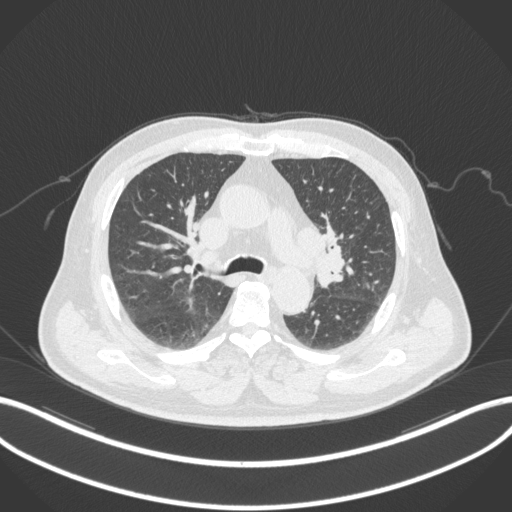
Chest CT, one axial slice. Reconstruction kernel B31f. Lung window (W 1500 / L -600 HU). 1 mm slice thickness. 512 × 512 image matrix, field of view 400 × 400 mm. Male patient, age 67 years. Case-level facts recorded for this patient, not image findings: clinical TNM (as recorded): T2a N1 M0; histopathological grade: G3.
Structures marked on this image (rectangle marked by the reading radiologist):
- lung tumour (recorded histology: adenocarcinoma): box from (x=313, y=246) to (x=350, y=291) px